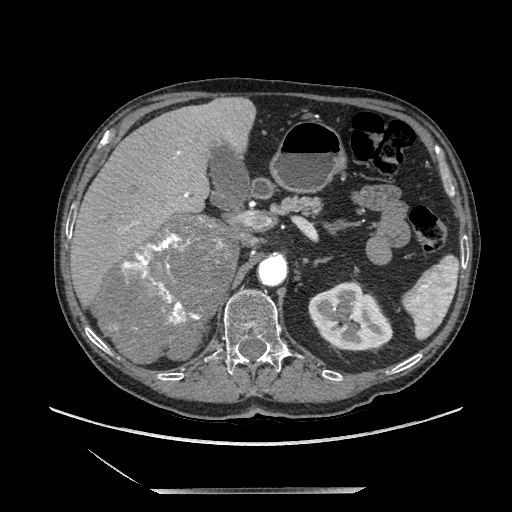
Contrast-enhanced abdominal CT, one axial slice. Soft-tissue window (W 400 / L 40 HU). 512 × 512 image matrix, field of view 420 × 420 mm. Male patient. Case-level facts recorded for this patient, not image findings: diagnosis: adrenocortical carcinoma; tumour side: right adrenal; tumour size at pathology: 16 cm; Ki-67 index: 17 %; stage (as recorded): 3.
Structures marked on this image (semi-automatic segmentation, software-assisted and operator-edited):
- mass: bounding box [x1, y1, x2, y2] px = [94, 215, 237, 361]